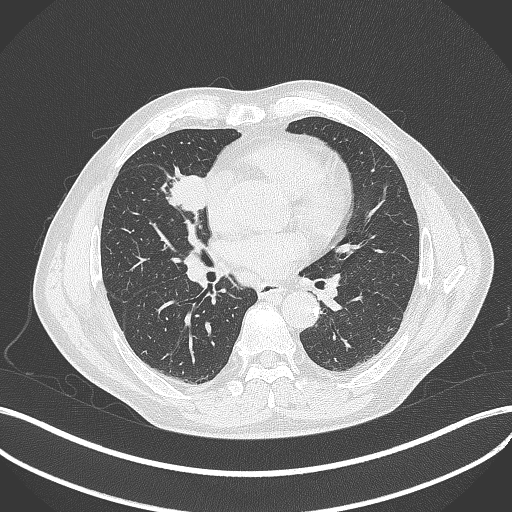
Chest CT, one axial slice. Position 195 of 429 along the scan axis. 120 kVp. Lung window (W 1500 / L -600 HU). 512 × 512 image matrix, field of view 400 × 400 mm. Patient: male, 61 years. From the clinical record (not read from this slice): clinical TNM (as recorded): T2b N1 M0.
Structures marked on this image (rectangle marked by the reading radiologist):
- lung tumour (recorded histology: squamous cell carcinoma): bounding box (x1, y1, x2, y2) in pixels: (160, 164, 208, 221)